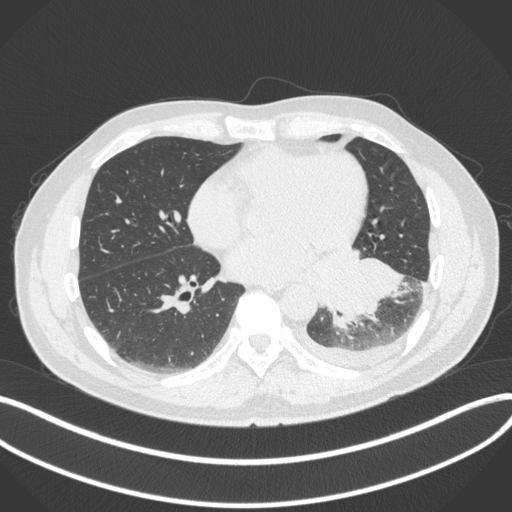
Chest CT, one axial slice. Position 147 of 350 along the scan axis. Lung window (W 1500 / L -600 HU). 1 mm slice thickness. 512 × 512 image matrix, field of view 400 × 400 mm. Male patient, age 58 years. From the clinical record (not read from this slice): clinical TNM (as recorded): T3 N1 M1b; histopathological grade: G3.
Outlined on this slice (rectangle marked by the reading radiologist):
- lung tumour (recorded histology: small cell carcinoma): box from (x=333, y=252) to (x=405, y=339) px